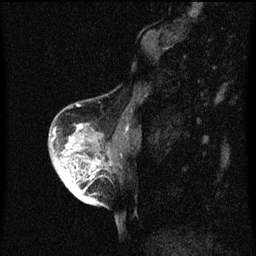
Breast MRI (dynamic contrast-enhanced), one sagittal slice; slice 21 of 60 in the series (ordered by position); dynamic contrast-enhanced series, image 2 of 3 at this slice position (ordered by acquisition); 1.5 T; TE 4.2 ms, TR 8 ms; 2 mm slice thickness; 256 × 256 image matrix, field of view 180 × 180 mm. Female patient, age 56 years.
Structures marked on this image (semi-automatic segmentation, software-assisted and operator-edited):
- analysis volume of interest (the breast-tissue region the enhancement analysis was run in; not a lesion): bounding box (x1, y1, x2, y2) in pixels: (54, 122, 114, 199)
- tumour enhancement mask (voxels above the 70 % enhancement threshold inside the analysis volume of interest): (63, 126, 101, 199)